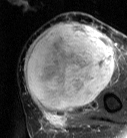
MRI of an extremity soft-tissue mass, one axial slice; position 32 of 87 along the scan axis; T2-weighted fat-saturated; MR volume resampled by the dataset authors to the PET/CT grid (not the native acquisition matrix); 3.27 mm slice thickness; 127 × 138 image matrix. Female patient. From the clinical record (not read from this slice): histological type: pleiomorphic leiomyosarcoma; grade: high; site of the primary tumour: left biceps.
Annotated regions visible in this slice (expert contour drawn on MRI and transferred to this co-registered scan by the dataset authors):
- gross tumour volume including surrounding oedema: bounding box <24,21,114,113> (left, top, right, bottom; pixels)
- gross tumour volume (mass): <24,23,114,111>